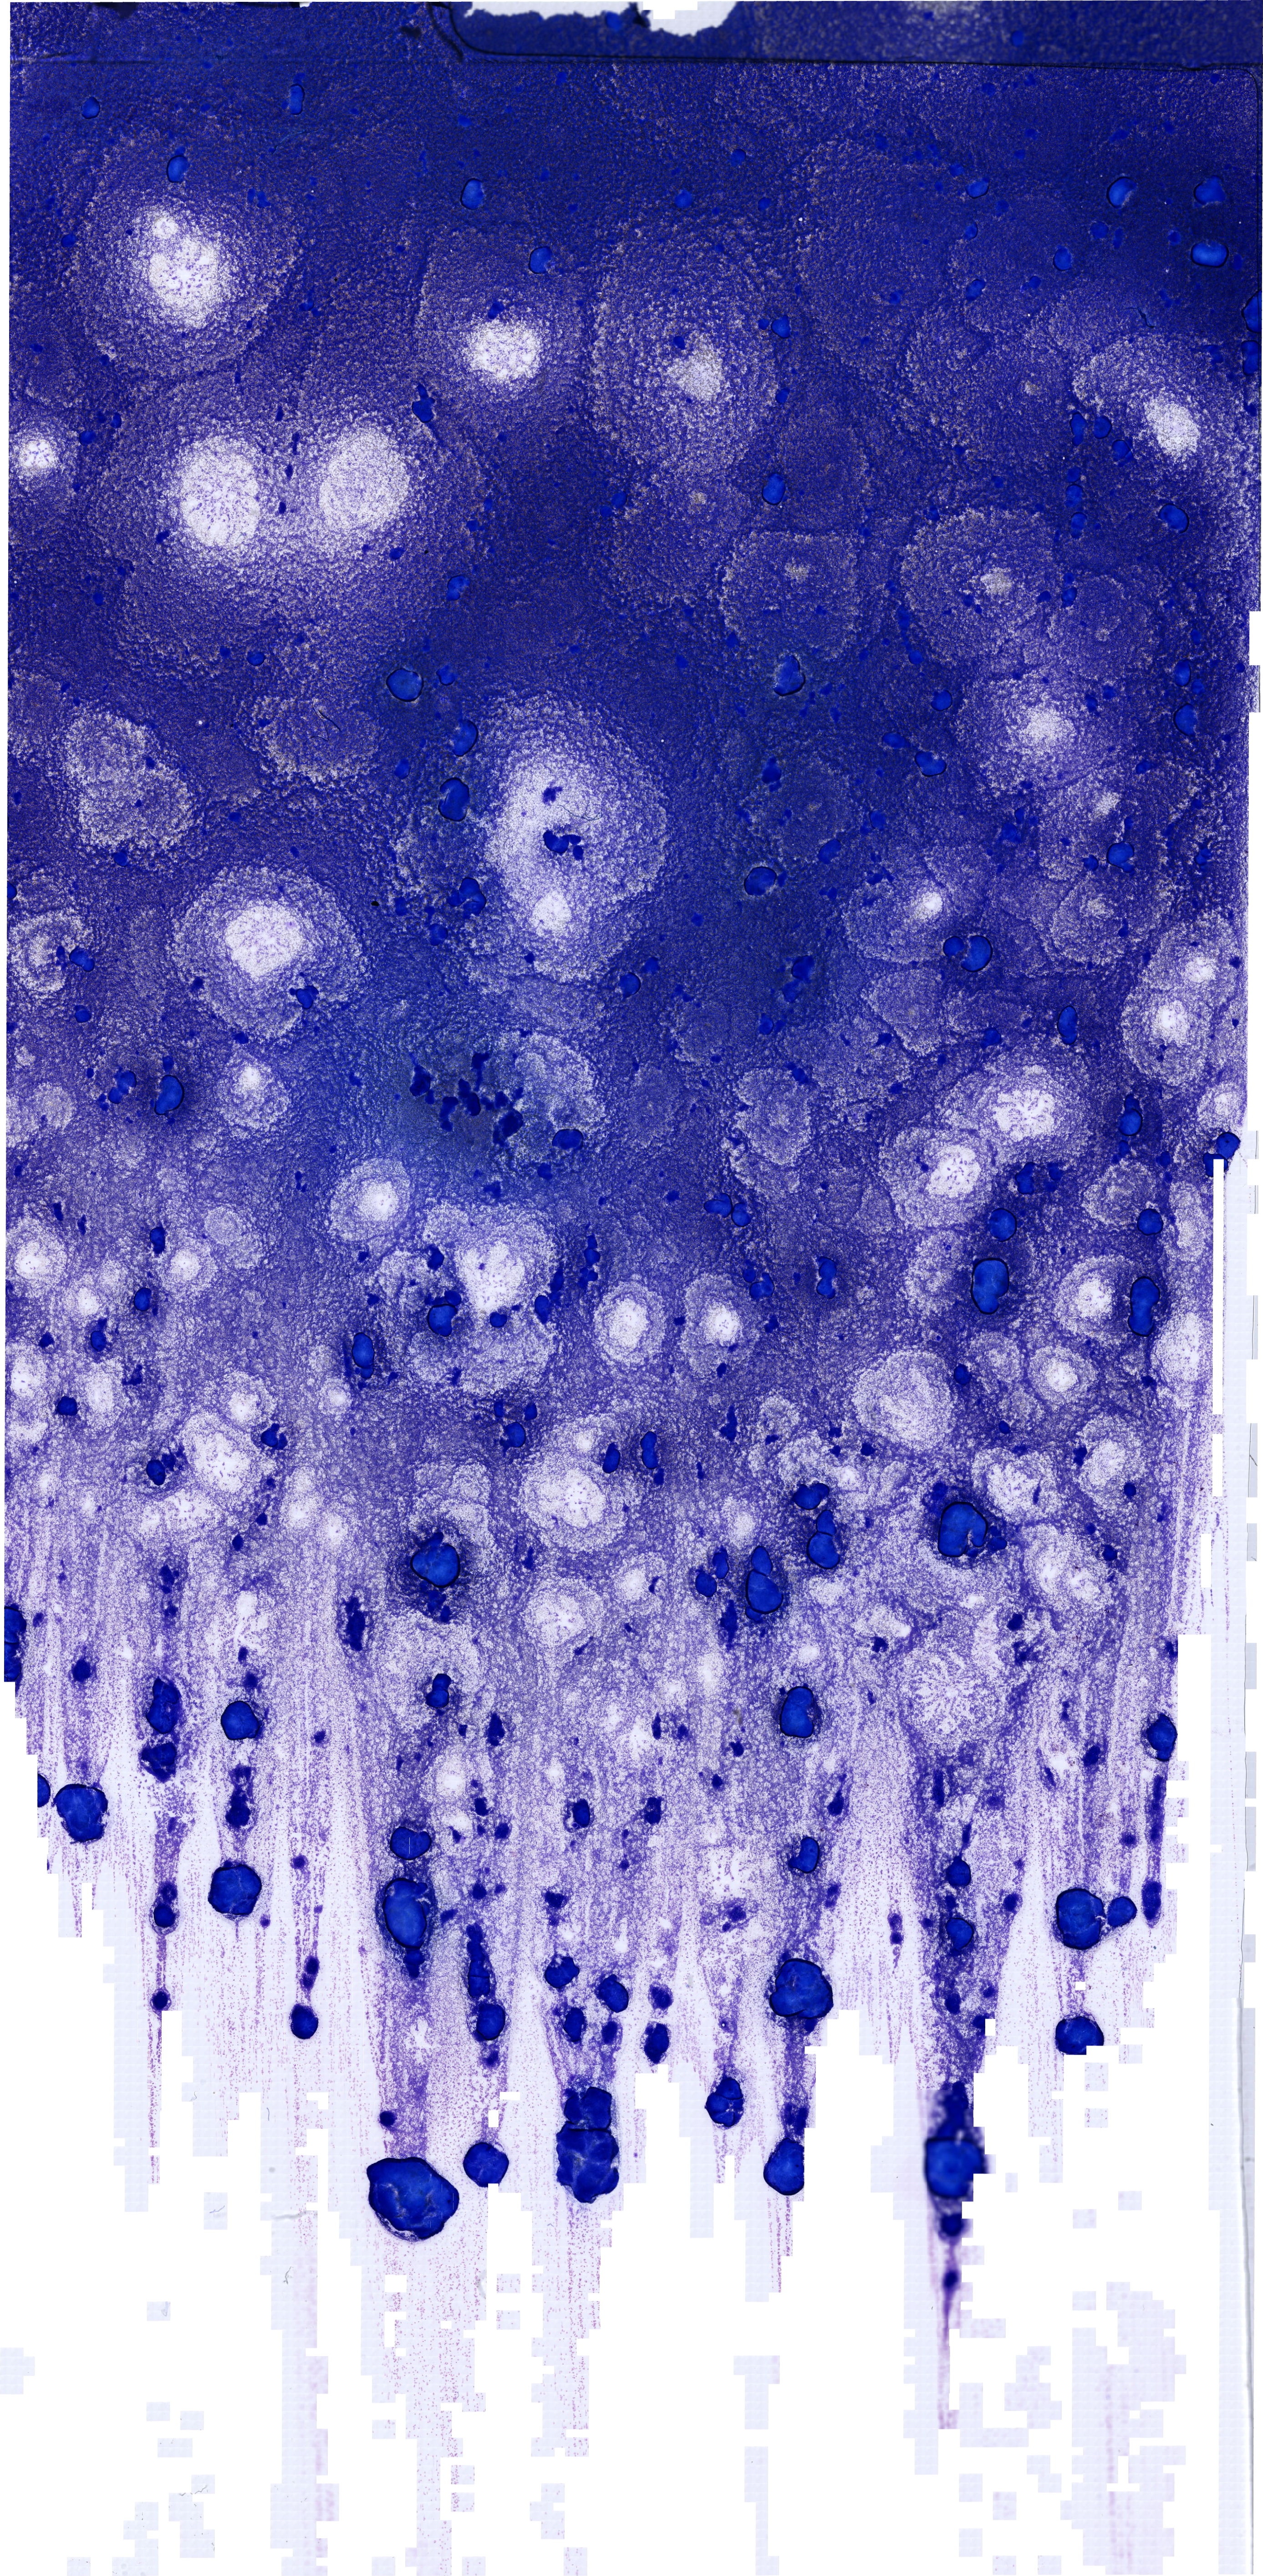
May-Grünwald-Giemsa (MGG)-stained marrow aspirate smear (whole slide), low-resolution overview of the scanned area, about 21.7 x 44.2 mm. Female patient.
• diagnosis: T Acute Lymphoblastic Leukemia